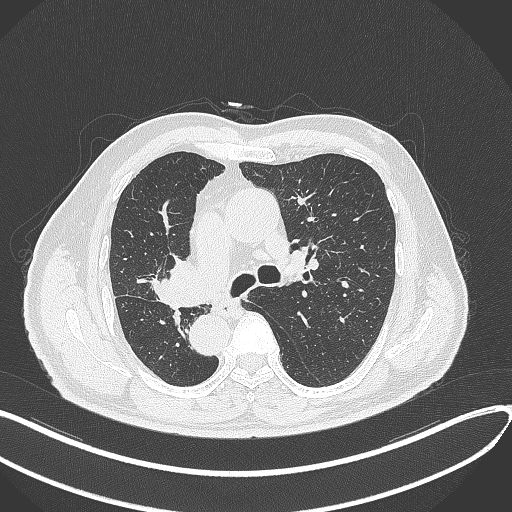
Chest CT, one axial slice; slice 187 of 300 in the series (ordered by position); reconstruction kernel B70f; lung window (W 1500 / L -600 HU); 1 mm slice thickness; 512 × 512 image matrix. Patient: male, 67 years. From the clinical record (not read from this slice): clinical TNM (as recorded): T2a N0 M0.
Annotated regions visible in this slice (bounding box drawn by a radiologist):
- lung tumour (recorded histology: squamous cell carcinoma): bounding box [x1, y1, x2, y2] px = [144, 249, 205, 311]